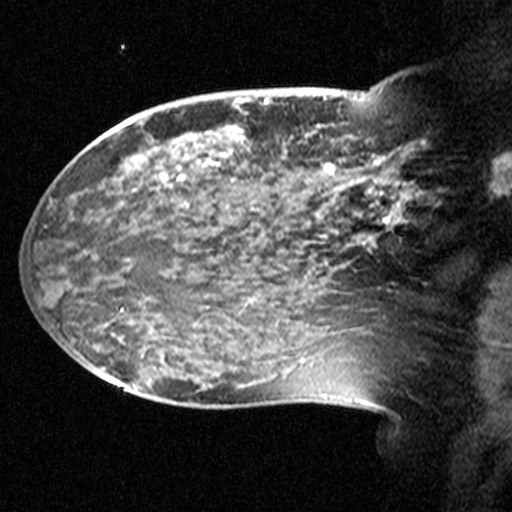
Breast MRI (dynamic contrast-enhanced), one sagittal slice; slice 16 of 44 in the series (ordered by position); dynamic contrast-enhanced study with each time point stored as its own series, time point 2 of 3 at this slice position (early post-contrast, ordered by acquisition time); 1.5 T; TE 4.5 ms, TR 11 ms; 512 × 512 image matrix. Patient: female, 38 years. Case-level facts recorded for this patient, not image findings: setting: breast cancer imaged before/during neoadjuvant chemotherapy; receptor status: HR-positive, HER2-negative.
Annotated regions visible in this slice (semi-automatically segmented with operator editing):
- analysis volume of interest (the breast-tissue region the enhancement analysis was run in; not a lesion): bounding box (x1, y1, x2, y2) in pixels: (124, 106, 405, 245)
- tumour enhancement mask (voxels above the 90 % enhancement threshold inside the analysis volume of interest): (162, 162, 397, 224)